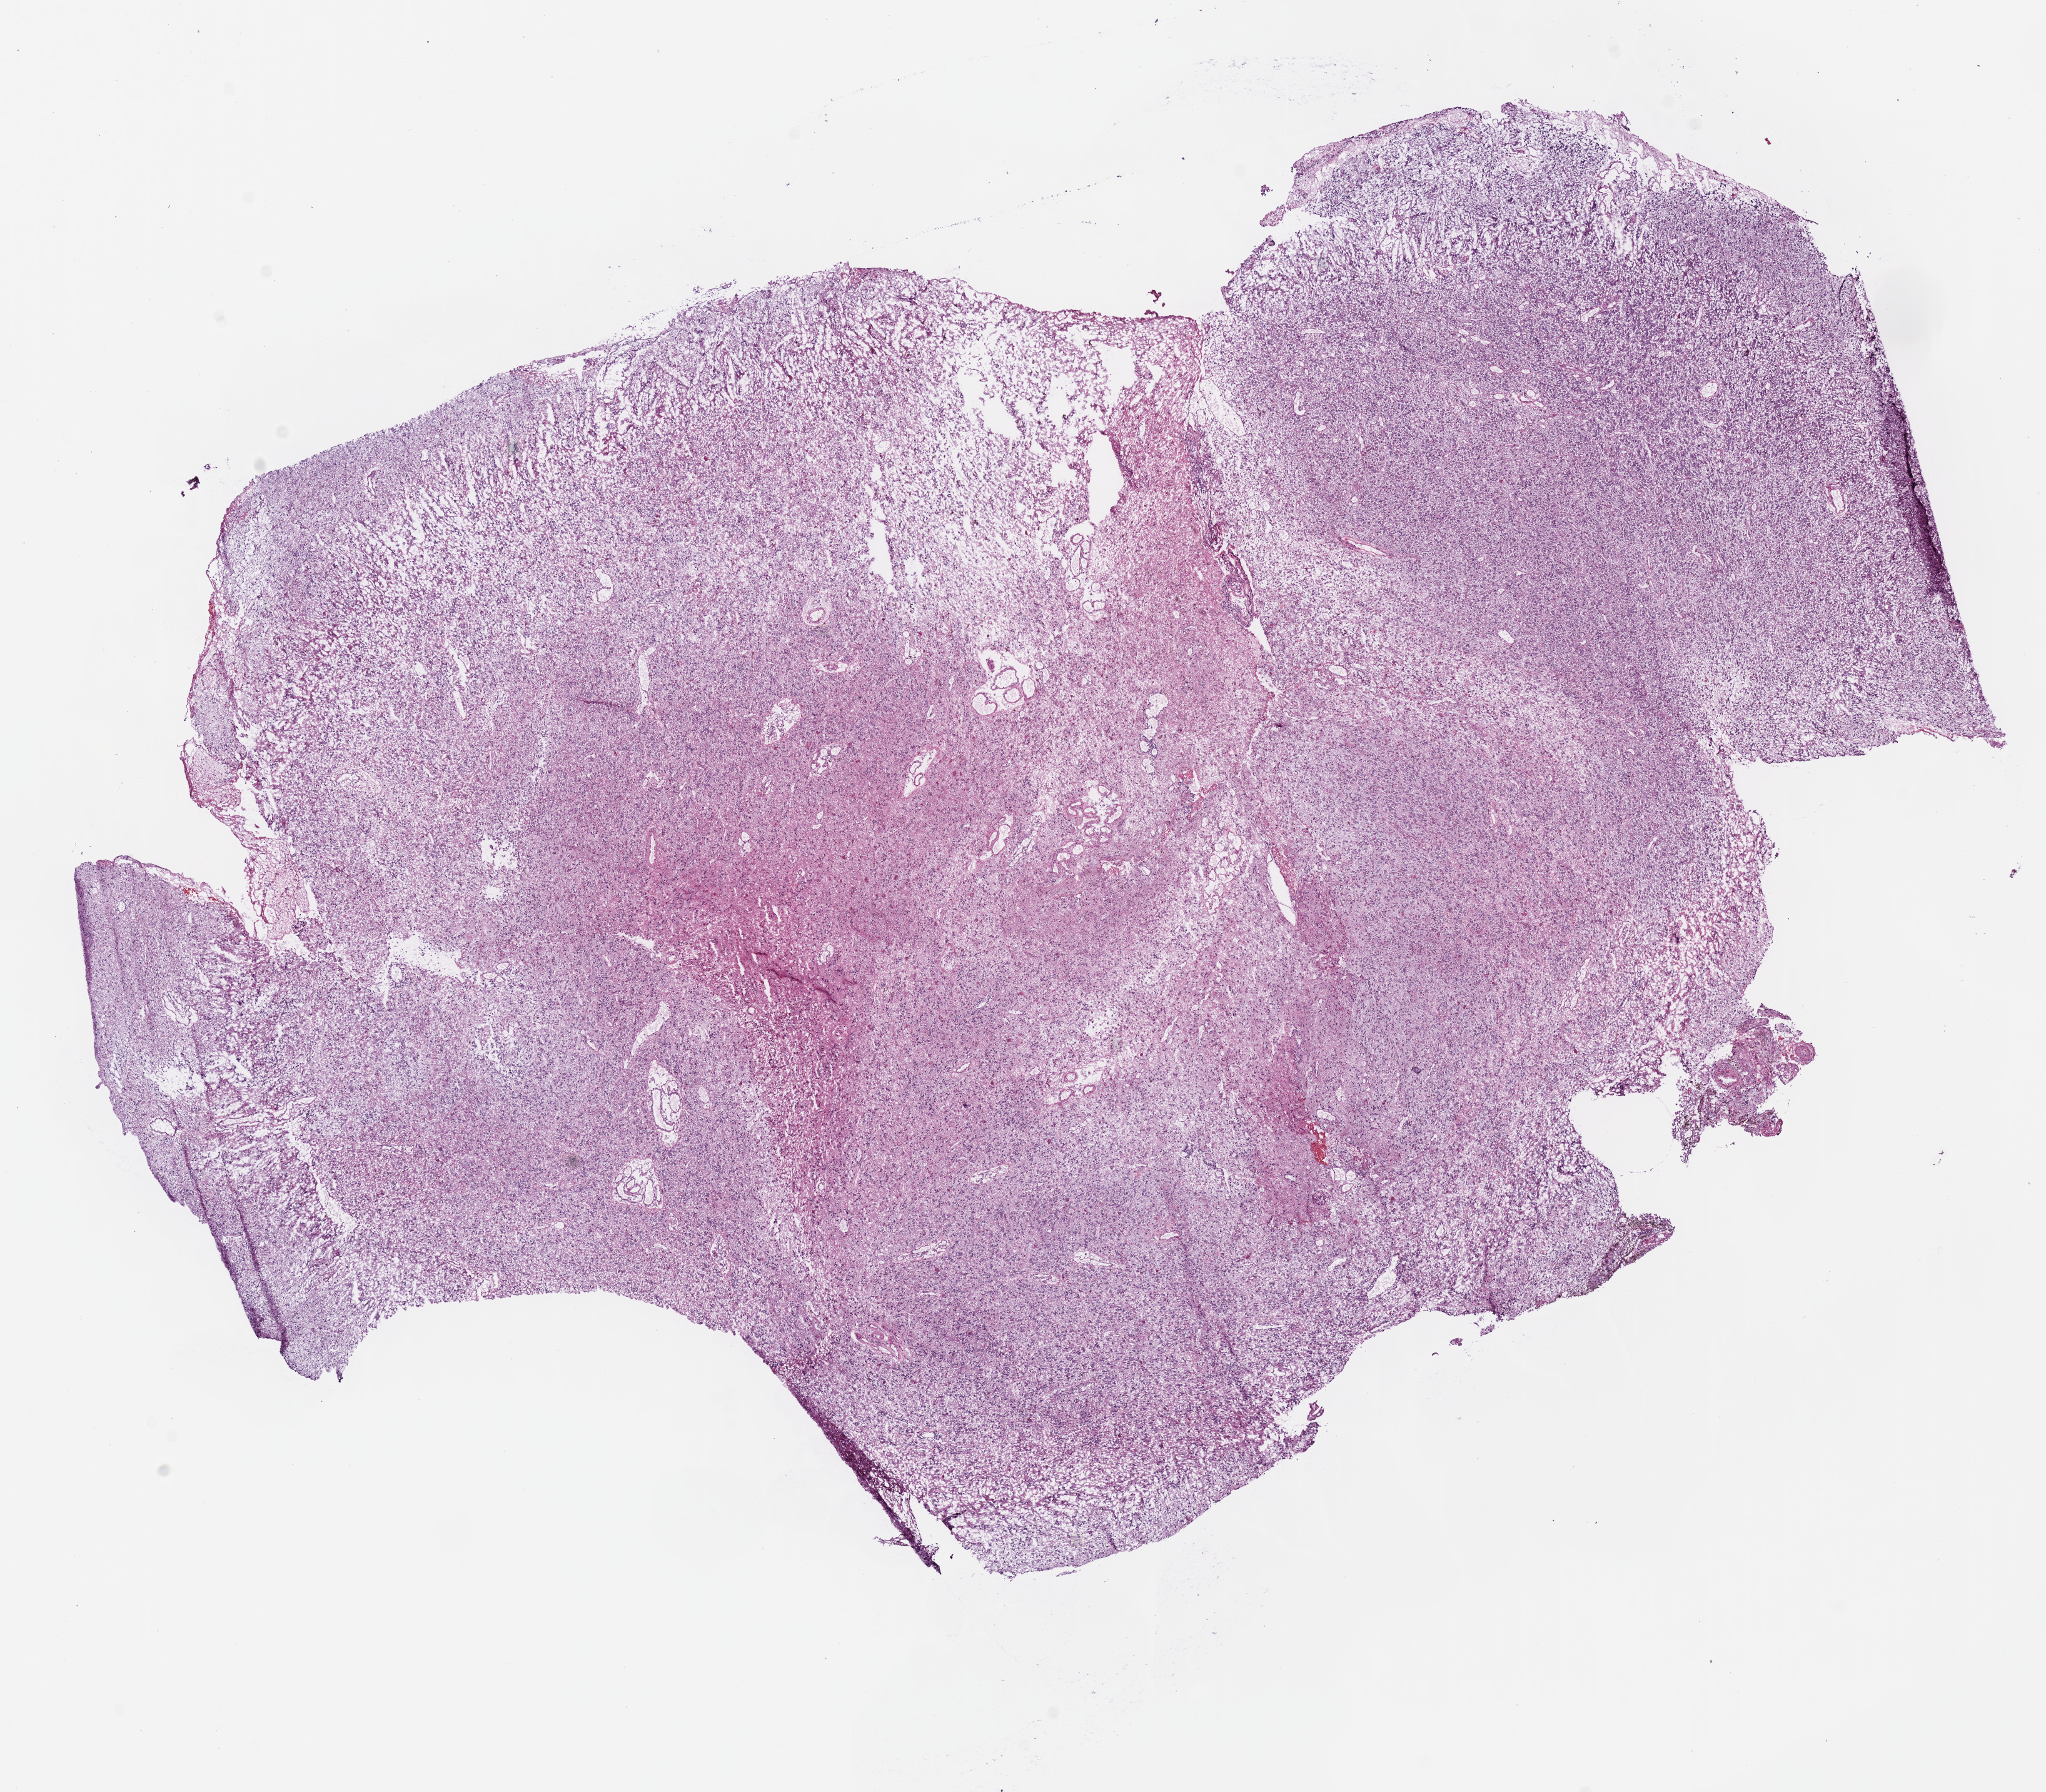
Digitized H&E-stained tissue section (whole slide) — whole scanned area (about 12.9 x 11.3 mm) shown as a low-resolution overview. Frozen section. Sample: primary tumour, brain. Patient: male, age at initial diagnosis 75 years. Histologic grade: G3 (poorly differentiated). Composition of this section per pathologist review: tumour cells 100%, tumour nuclei 85%, normal cells 0%, stromal cells 0%, necrosis 0%.
Pathologic diagnosis: Oligodendroglioma, anaplastic. Laterality: right.